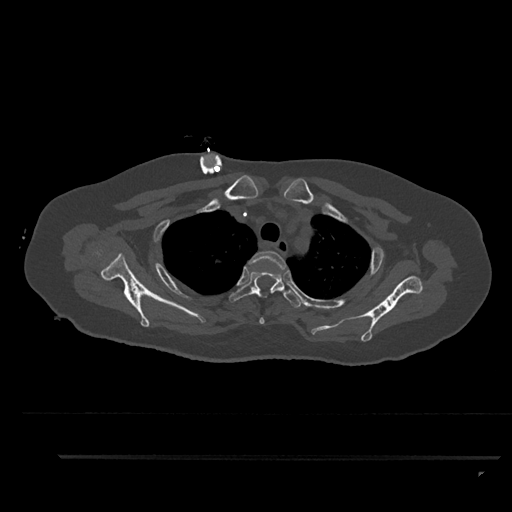
CT including the spine, one axial slice. Bone window (W 1800 / L 400 HU). 0.5 mm slice thickness. 512 × 512 image matrix, field of view 408 × 408 mm. Female patient, age 44 years. From the clinical record (not read from this slice): primary cancer: renal.
Outlined on this slice (semi-automatically segmented with operator editing):
- T2 vertebra: bounding box <248,251,287,324> (left, top, right, bottom; pixels)
- T3 vertebra: <229,270,303,308>